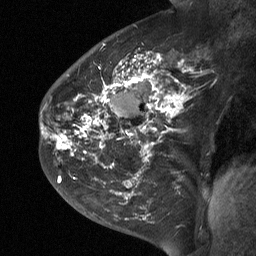
Breast MRI (dynamic contrast-enhanced), one sagittal slice. Position 37 of 64 along the scan axis. Dynamic contrast-enhanced study with each time point stored as its own series, time point 2 of 3 at this slice position (early post-contrast, ordered by acquisition time). 1.5 T. TE 4.8 ms, TR 27 ms. 2 mm slice thickness. 256 × 256 image matrix. Female patient, age 42 years. From the clinical record (not read from this slice): setting: breast cancer imaged before/during neoadjuvant chemotherapy; receptor status: triple-negative.
Structures marked on this image (semi-automatic segmentation, software-assisted and operator-edited):
- analysis volume of interest (the breast-tissue region the enhancement analysis was run in; not a lesion): box from (x=43, y=29) to (x=201, y=190) px
- tumour enhancement mask (voxels above the 90 % enhancement threshold inside the analysis volume of interest): (x=43, y=52)–(x=192, y=183)